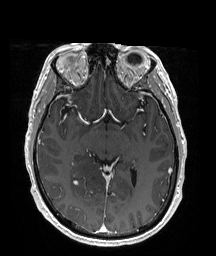
Brain MRI from a brain-tumour surgery series, one axial slice. Slice 105 of 176 in the series (ordered by position). T1-weighted post-contrast. 1 mm slice thickness. 216 × 256 image matrix, field of view 211 × 250 mm. Case-level facts recorded for this patient, not image findings: histopathology: Oligodendroglioma; WHO grade: 2; IDH mutation: yes.
Outlined on this slice (manually delineated by an expert):
- tumour: bounding box [x1, y1, x2, y2] px = [70, 150, 111, 205]